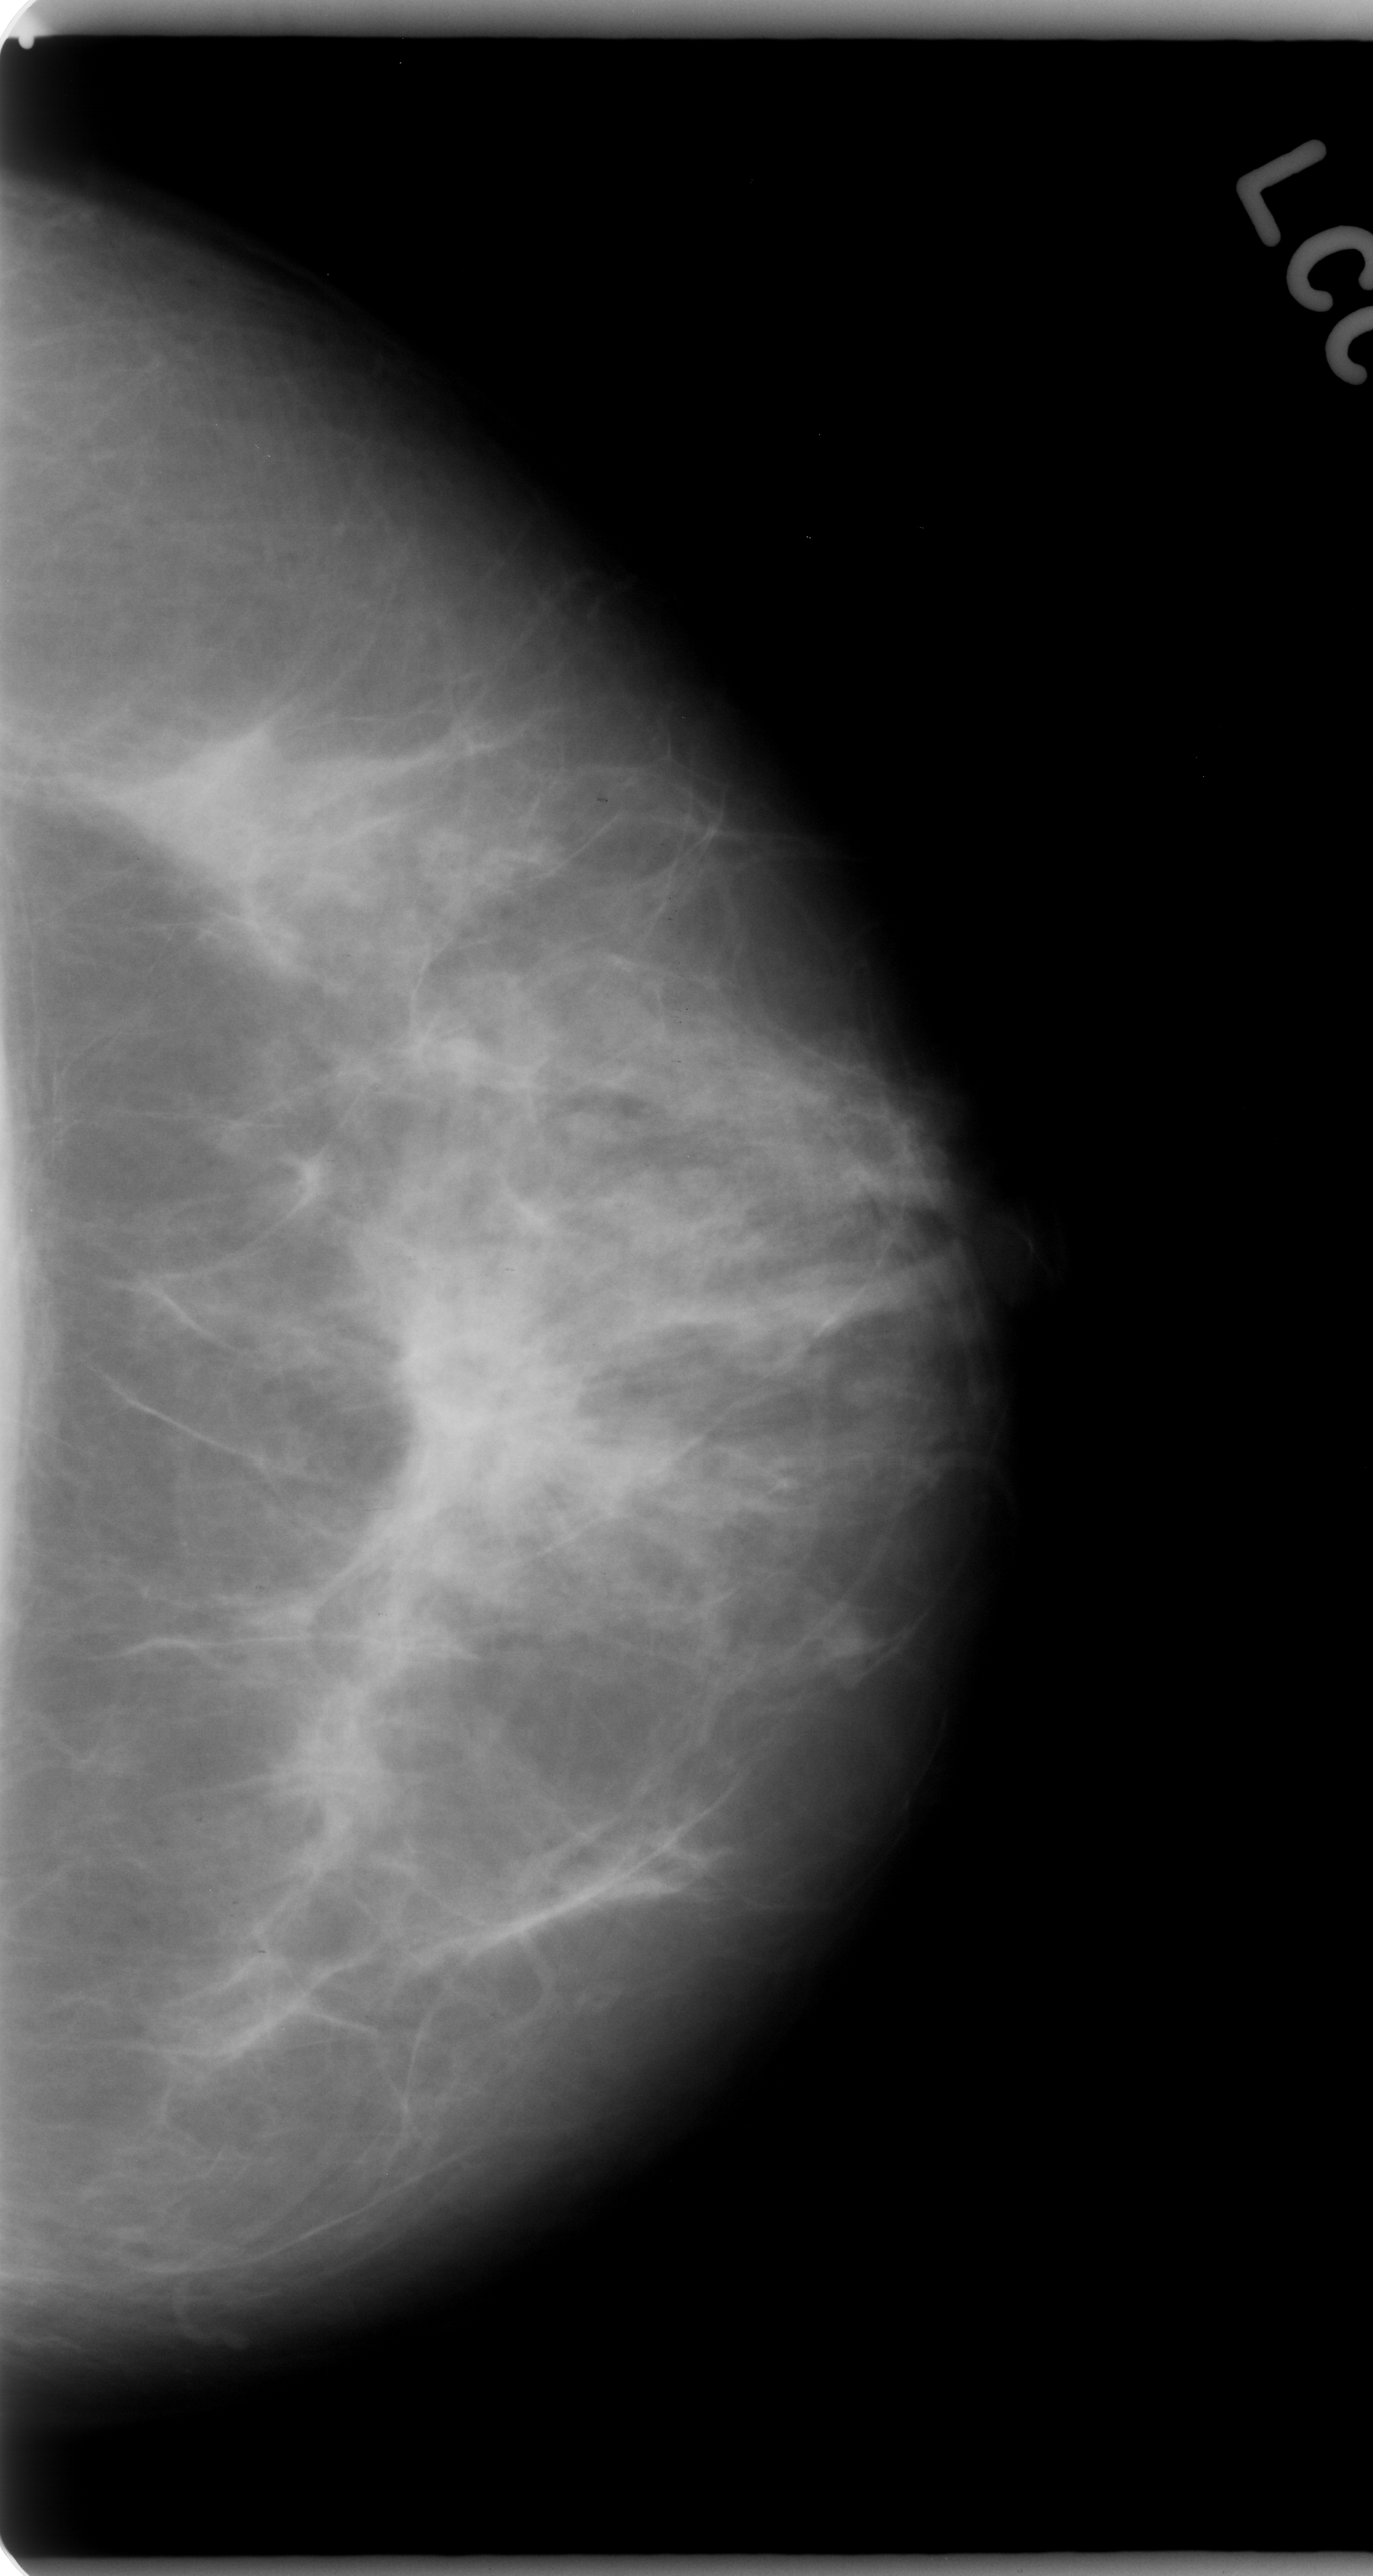
Digitized screen-film mammogram, left breast, craniocaudal (CC) view, breast composition: scattered fibroglandular densities (BI-RADS density category 2 of 4).
- Mass, shape architectural distortion, margins spiculated; BI-RADS assessment category 5; pathology (as recorded): malignant.